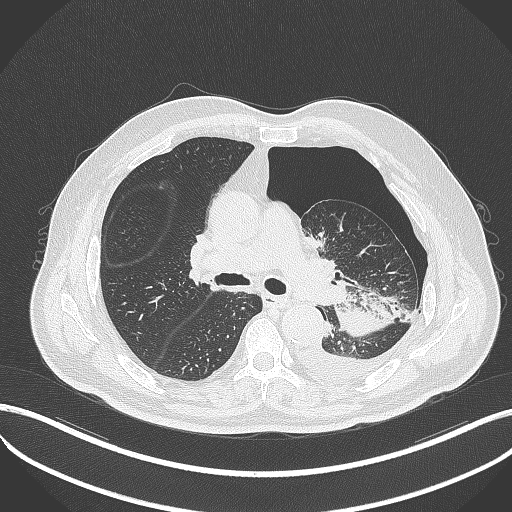
Chest CT, one axial slice; lung window (W 1500 / L -600 HU); 512 × 512 image matrix, field of view 400 × 400 mm. Male patient, age 76 years. From the clinical record (not read from this slice): clinical TNM (as recorded): T3 N0 M1b.
Outlined on this slice (bounding box drawn by a radiologist):
- lung tumour (recorded histology: adenocarcinoma): bounding box [x1, y1, x2, y2] px = [333, 300, 393, 338]